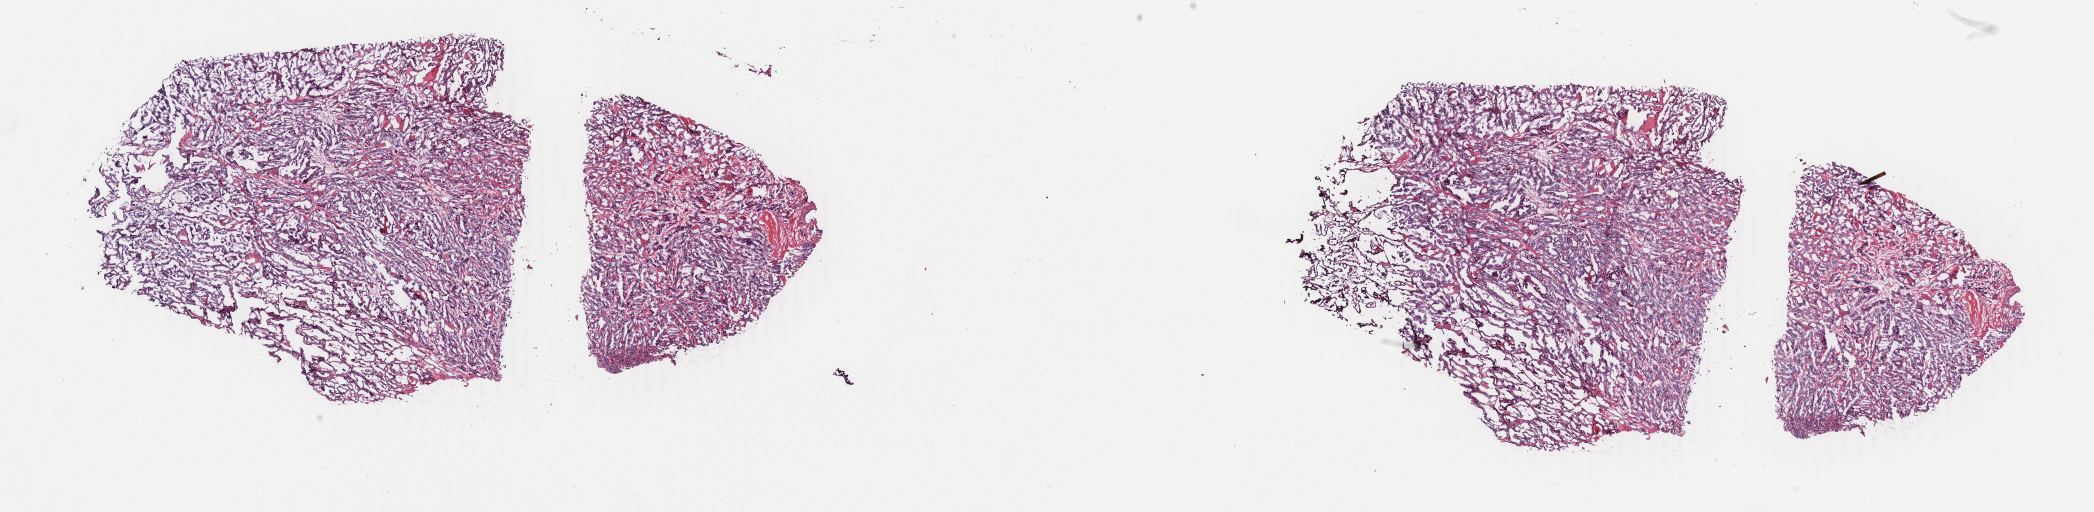
Digitized H&E-stained tissue section (whole slide) — whole scanned area (about 33.3 x 8.1 mm, slide scanned at 40x) shown as a low-resolution overview, frozen section, thyroid, primary tumour sample. Female patient; age at initial diagnosis 46 years. Pathologist review of this section (percent, as recorded): tumour cells 85%, tumour nuclei 80%, normal cells 0%, stromal cells 15%, necrosis 0%. Inflammatory infiltration, as recorded: lymphocyte infiltration 2%, monocyte infiltration 0%, neutrophil infiltration 0%.
Lymph nodes positive (case pathology): 0 of 5 examined. AJCC pathologic stage: I (6th edition). Diagnosis: Papillary adenocarcinoma, NOS.